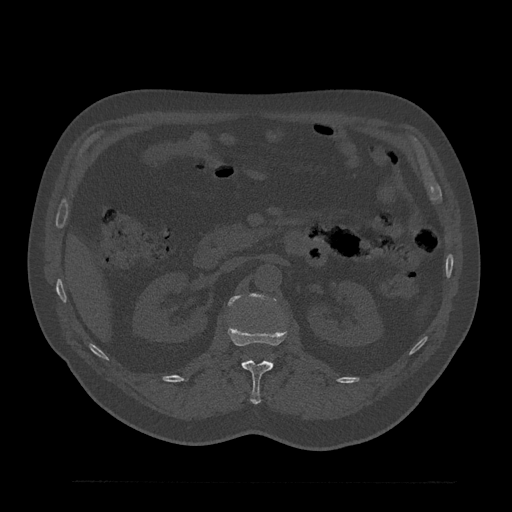
CT including the spine, one axial slice; position 148 of 797 along the scan axis; 120 kVp; bone window (W 1800 / L 400 HU); 512 × 512 image matrix, field of view 430 × 430 mm. Patient: male, 61 years. Case-level facts recorded for this patient, not image findings: primary cancer: prostate.
Outlined on this slice (semi-automatically segmented with operator editing):
- L1 vertebra: bounding box [x1, y1, x2, y2] px = [227, 324, 287, 405]
- L2 vertebra: [228, 295, 255, 306]